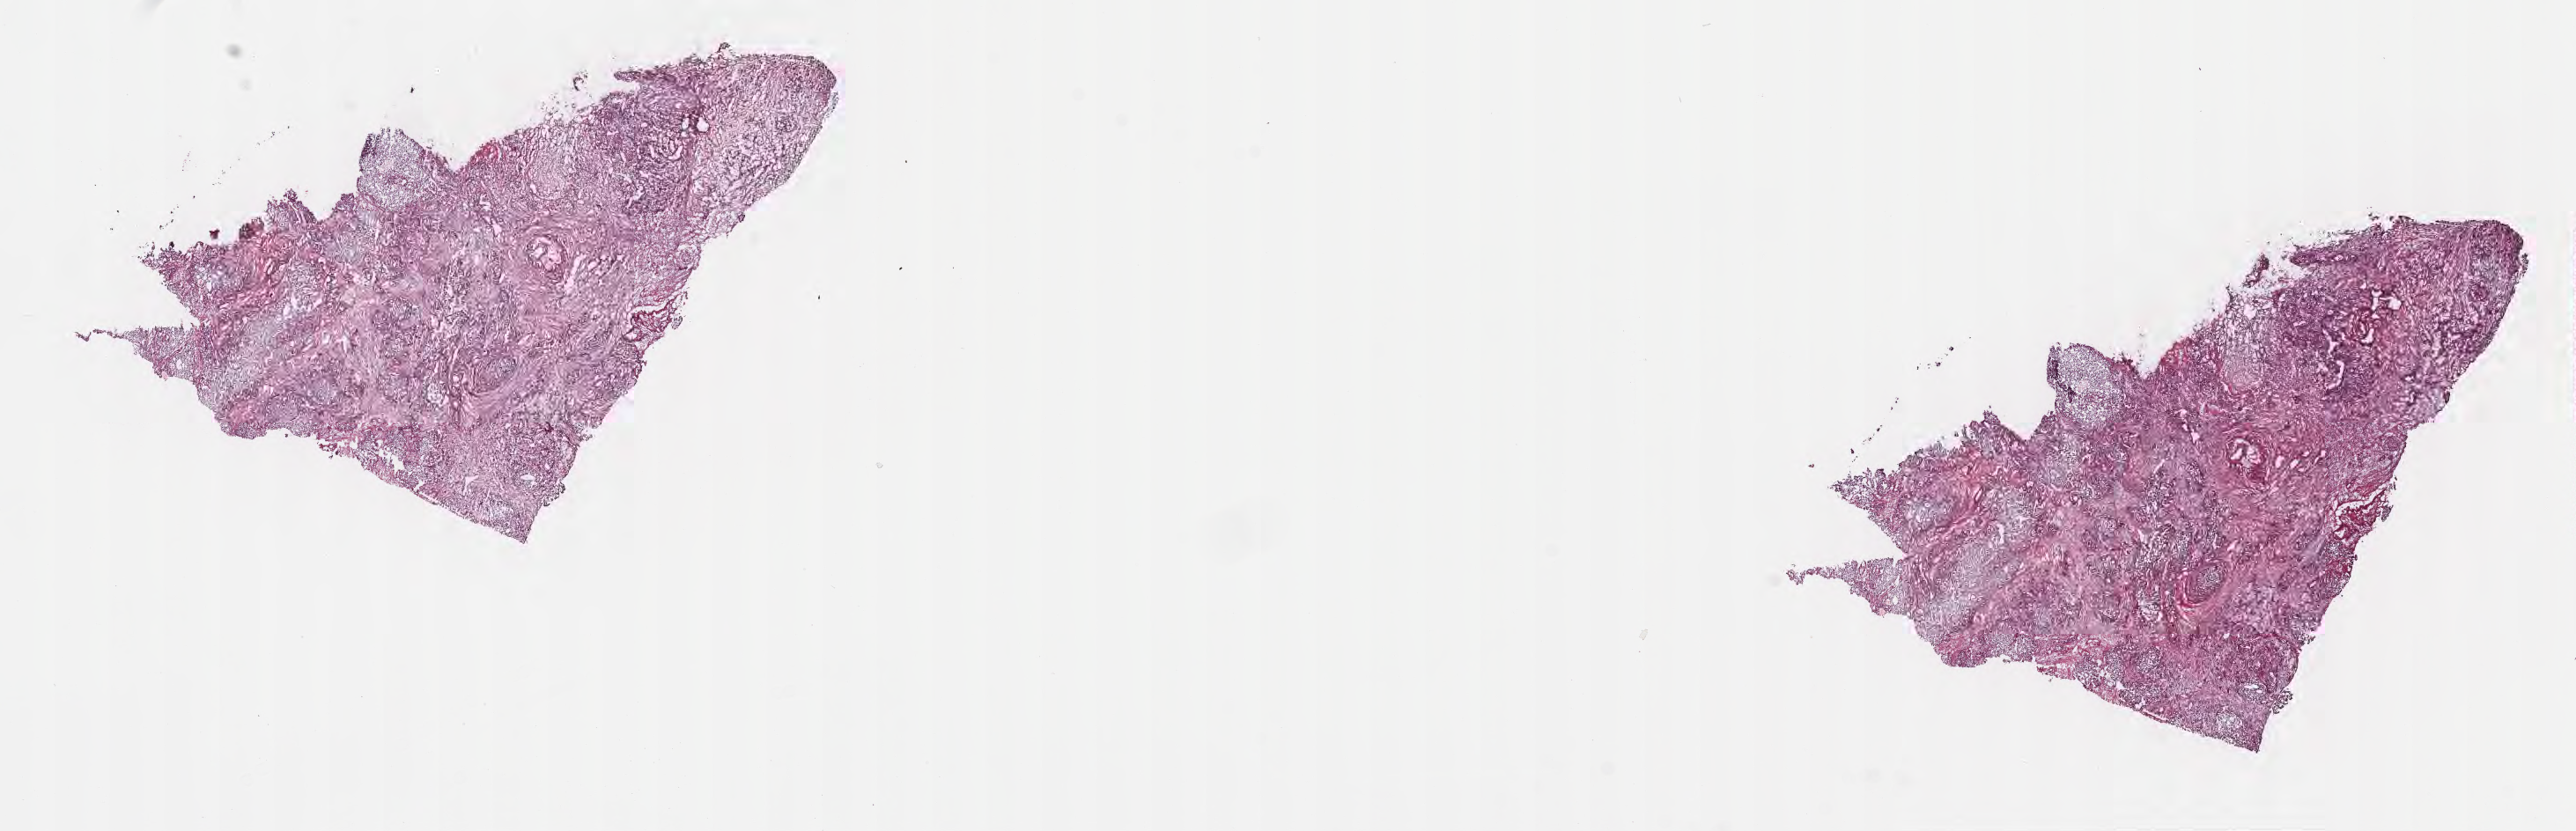
Hematoxylin and eosin (H&E) whole-slide image, whole scanned area (about 23.7 x 7.6 mm) shown as a low-resolution overview; cryosection; specimen: primary tumor; anatomic site: head of pancreas. Male, age 67 years at initial diagnosis.
Histologic diagnosis: Infiltrating duct carcinoma, NOS.